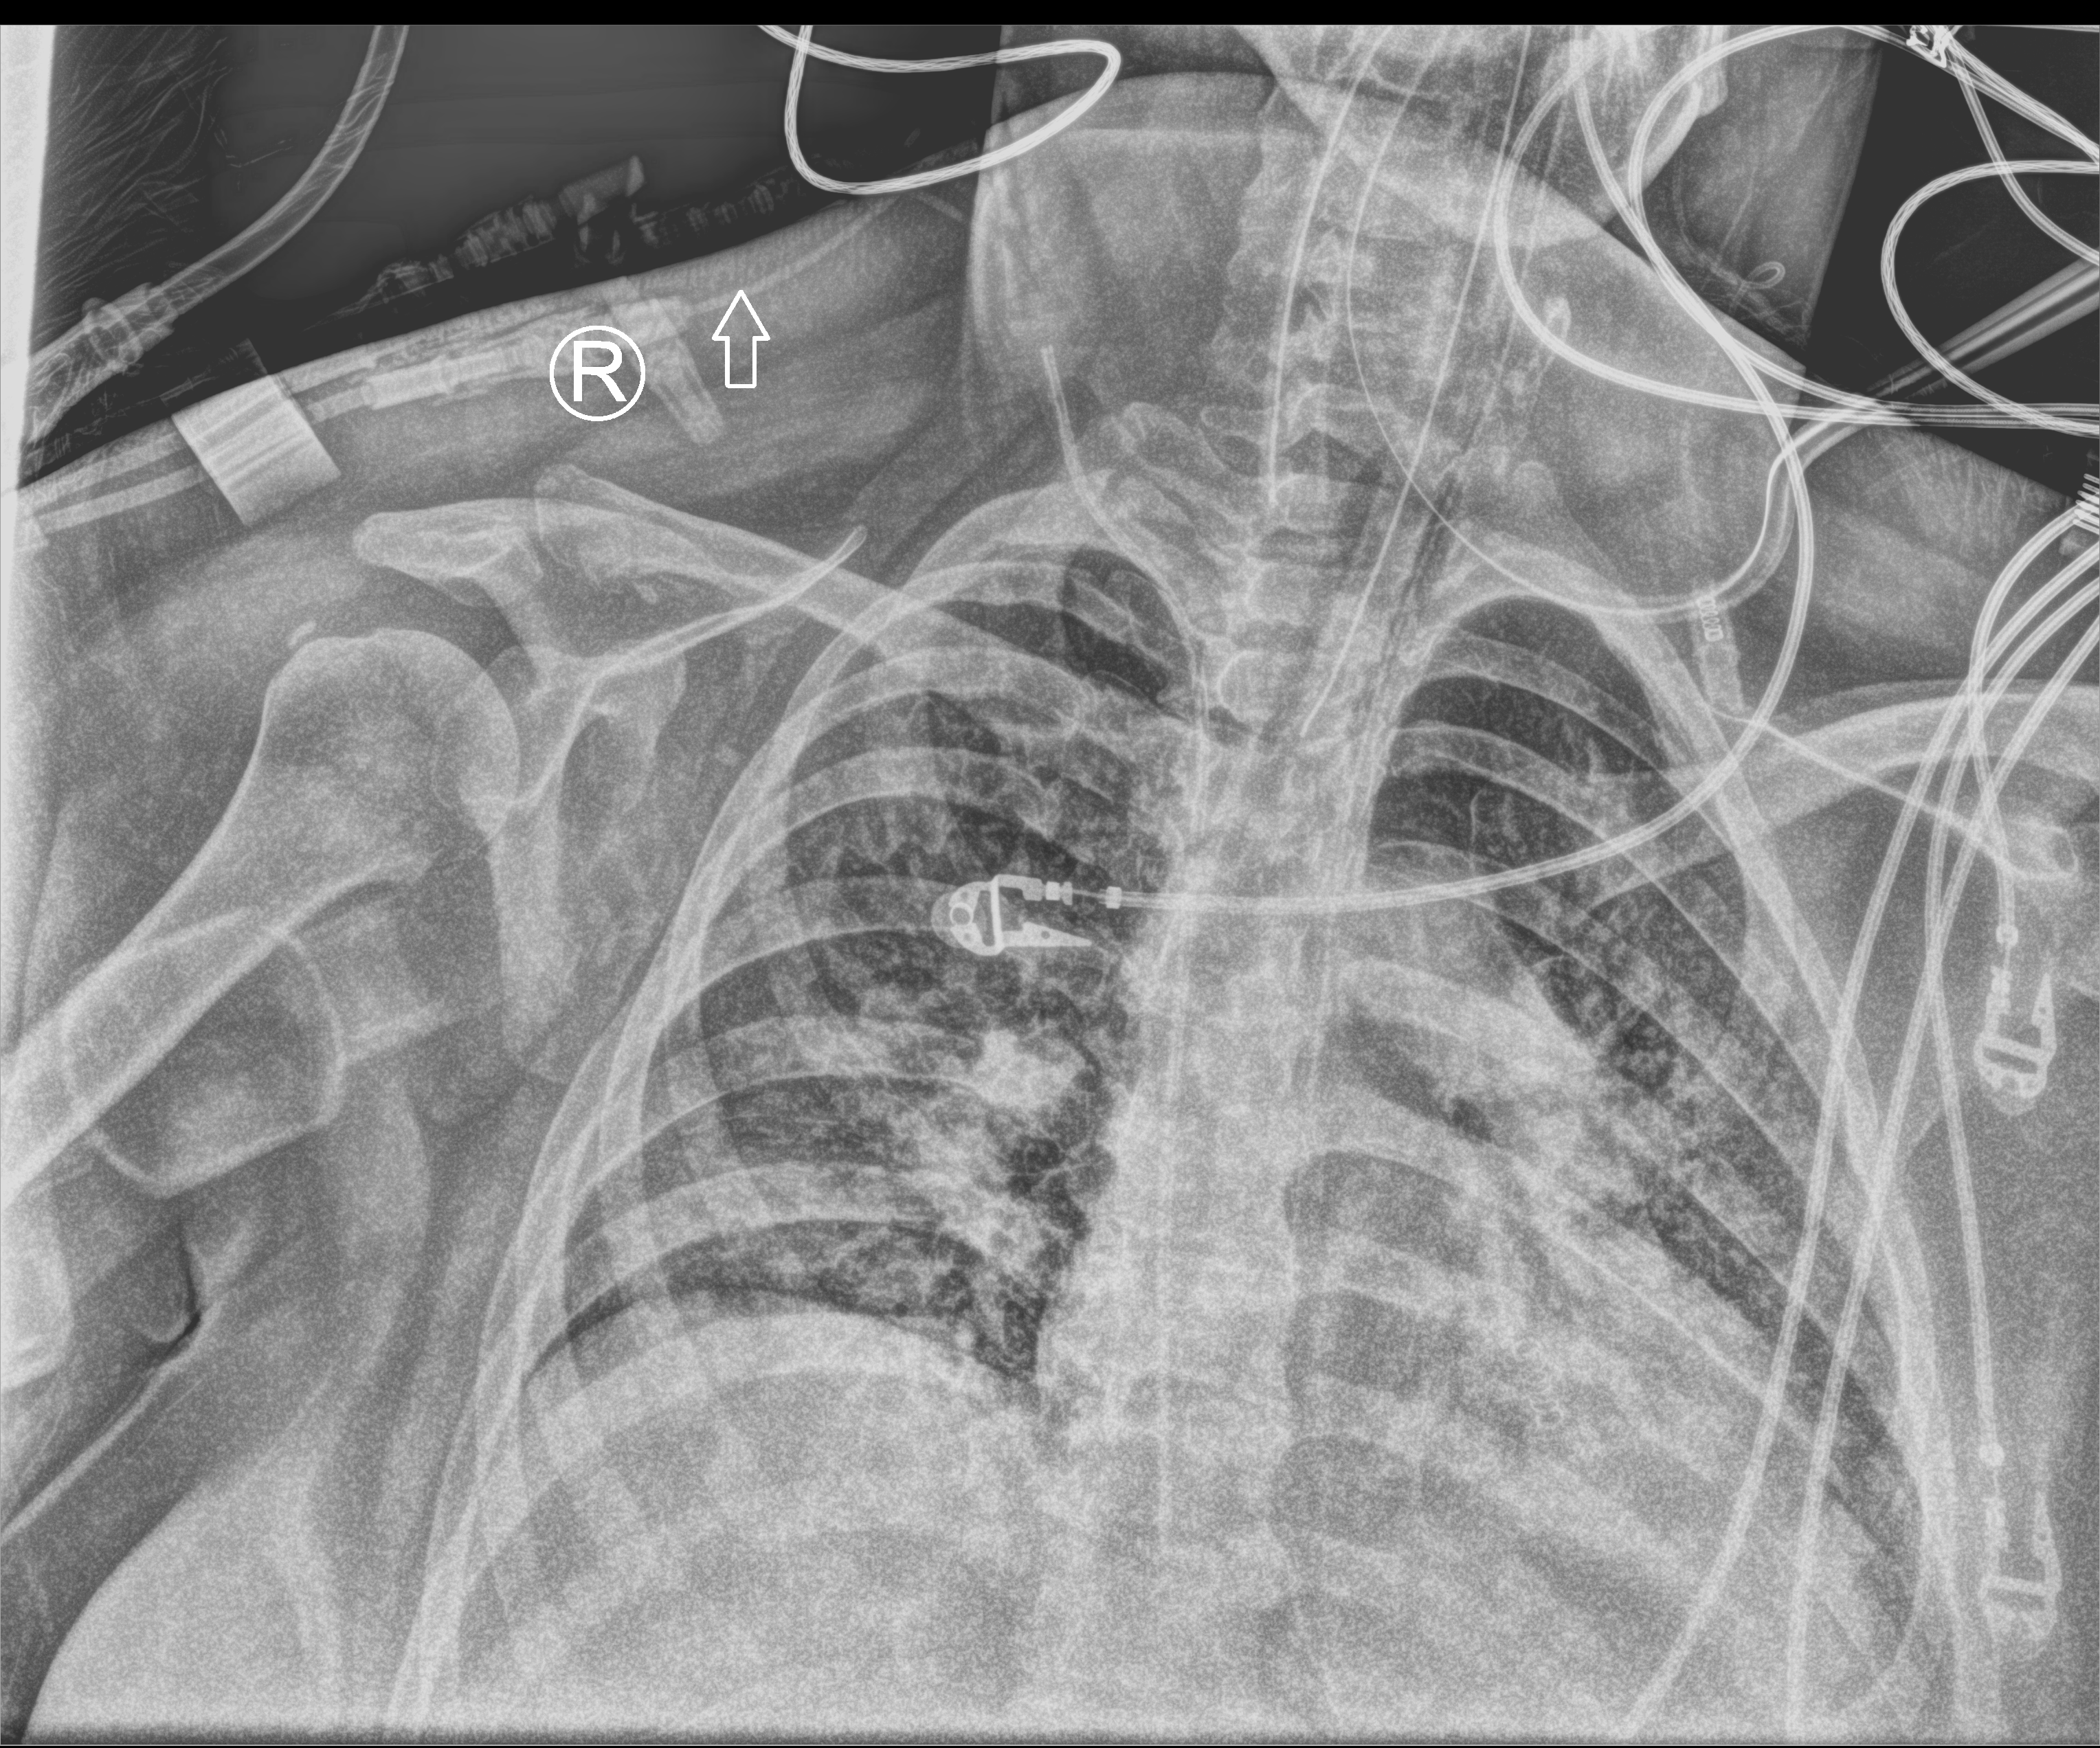
Bedside chest radiograph (computed radiography). Patient hospitalised with COVID-19; female, aged 18–59 years.
From the hospital-stay record, not from the radiograph (when in the stay this image was taken is not recorded): hypertension (admission record): no.